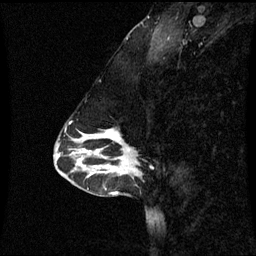
Breast MRI (dynamic contrast-enhanced), one sagittal slice. Position 24 of 60 along the scan axis. Dynamic contrast-enhanced series, image 2 of 3 at this slice position (ordered by acquisition). 1.5 T. TE 4.2 ms, TR 8.9 ms. 2 mm slice thickness. 256 × 256 image matrix, field of view 220 × 220 mm. Female patient, age 43 years. From the clinical record (not read from this slice): setting: breast cancer imaged before/during neoadjuvant chemotherapy; receptor status: HR-positive, HER2-negative.
Annotated regions visible in this slice (semi-automatically segmented with operator editing):
- analysis volume of interest (the breast-tissue region the enhancement analysis was run in; not a lesion): bounding box <84,130,140,171> (left, top, right, bottom; pixels)
- tumour enhancement mask (voxels above the 70 % enhancement threshold inside the analysis volume of interest): <105,130,129,151>